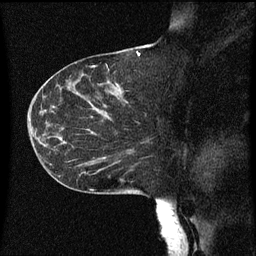
Breast MRI (dynamic contrast-enhanced), one sagittal slice; slice 31 of 60 in the series (ordered by position); dynamic contrast-enhanced series, image 2 of 3 at this slice position (ordered by acquisition); 1.5 T; TE 4.2 ms, TR 8 ms; 2 mm slice thickness; 256 × 256 image matrix, field of view 200 × 200 mm. Patient: female, 55 years.
Structures marked on this image (semi-automatic segmentation, software-assisted and operator-edited):
- analysis volume of interest (the breast-tissue region the enhancement analysis was run in; not a lesion): bounding box [x1, y1, x2, y2] px = [46, 124, 151, 183]
- tumour enhancement mask (voxels above the 70 % enhancement threshold inside the analysis volume of interest): [70, 152, 131, 181]